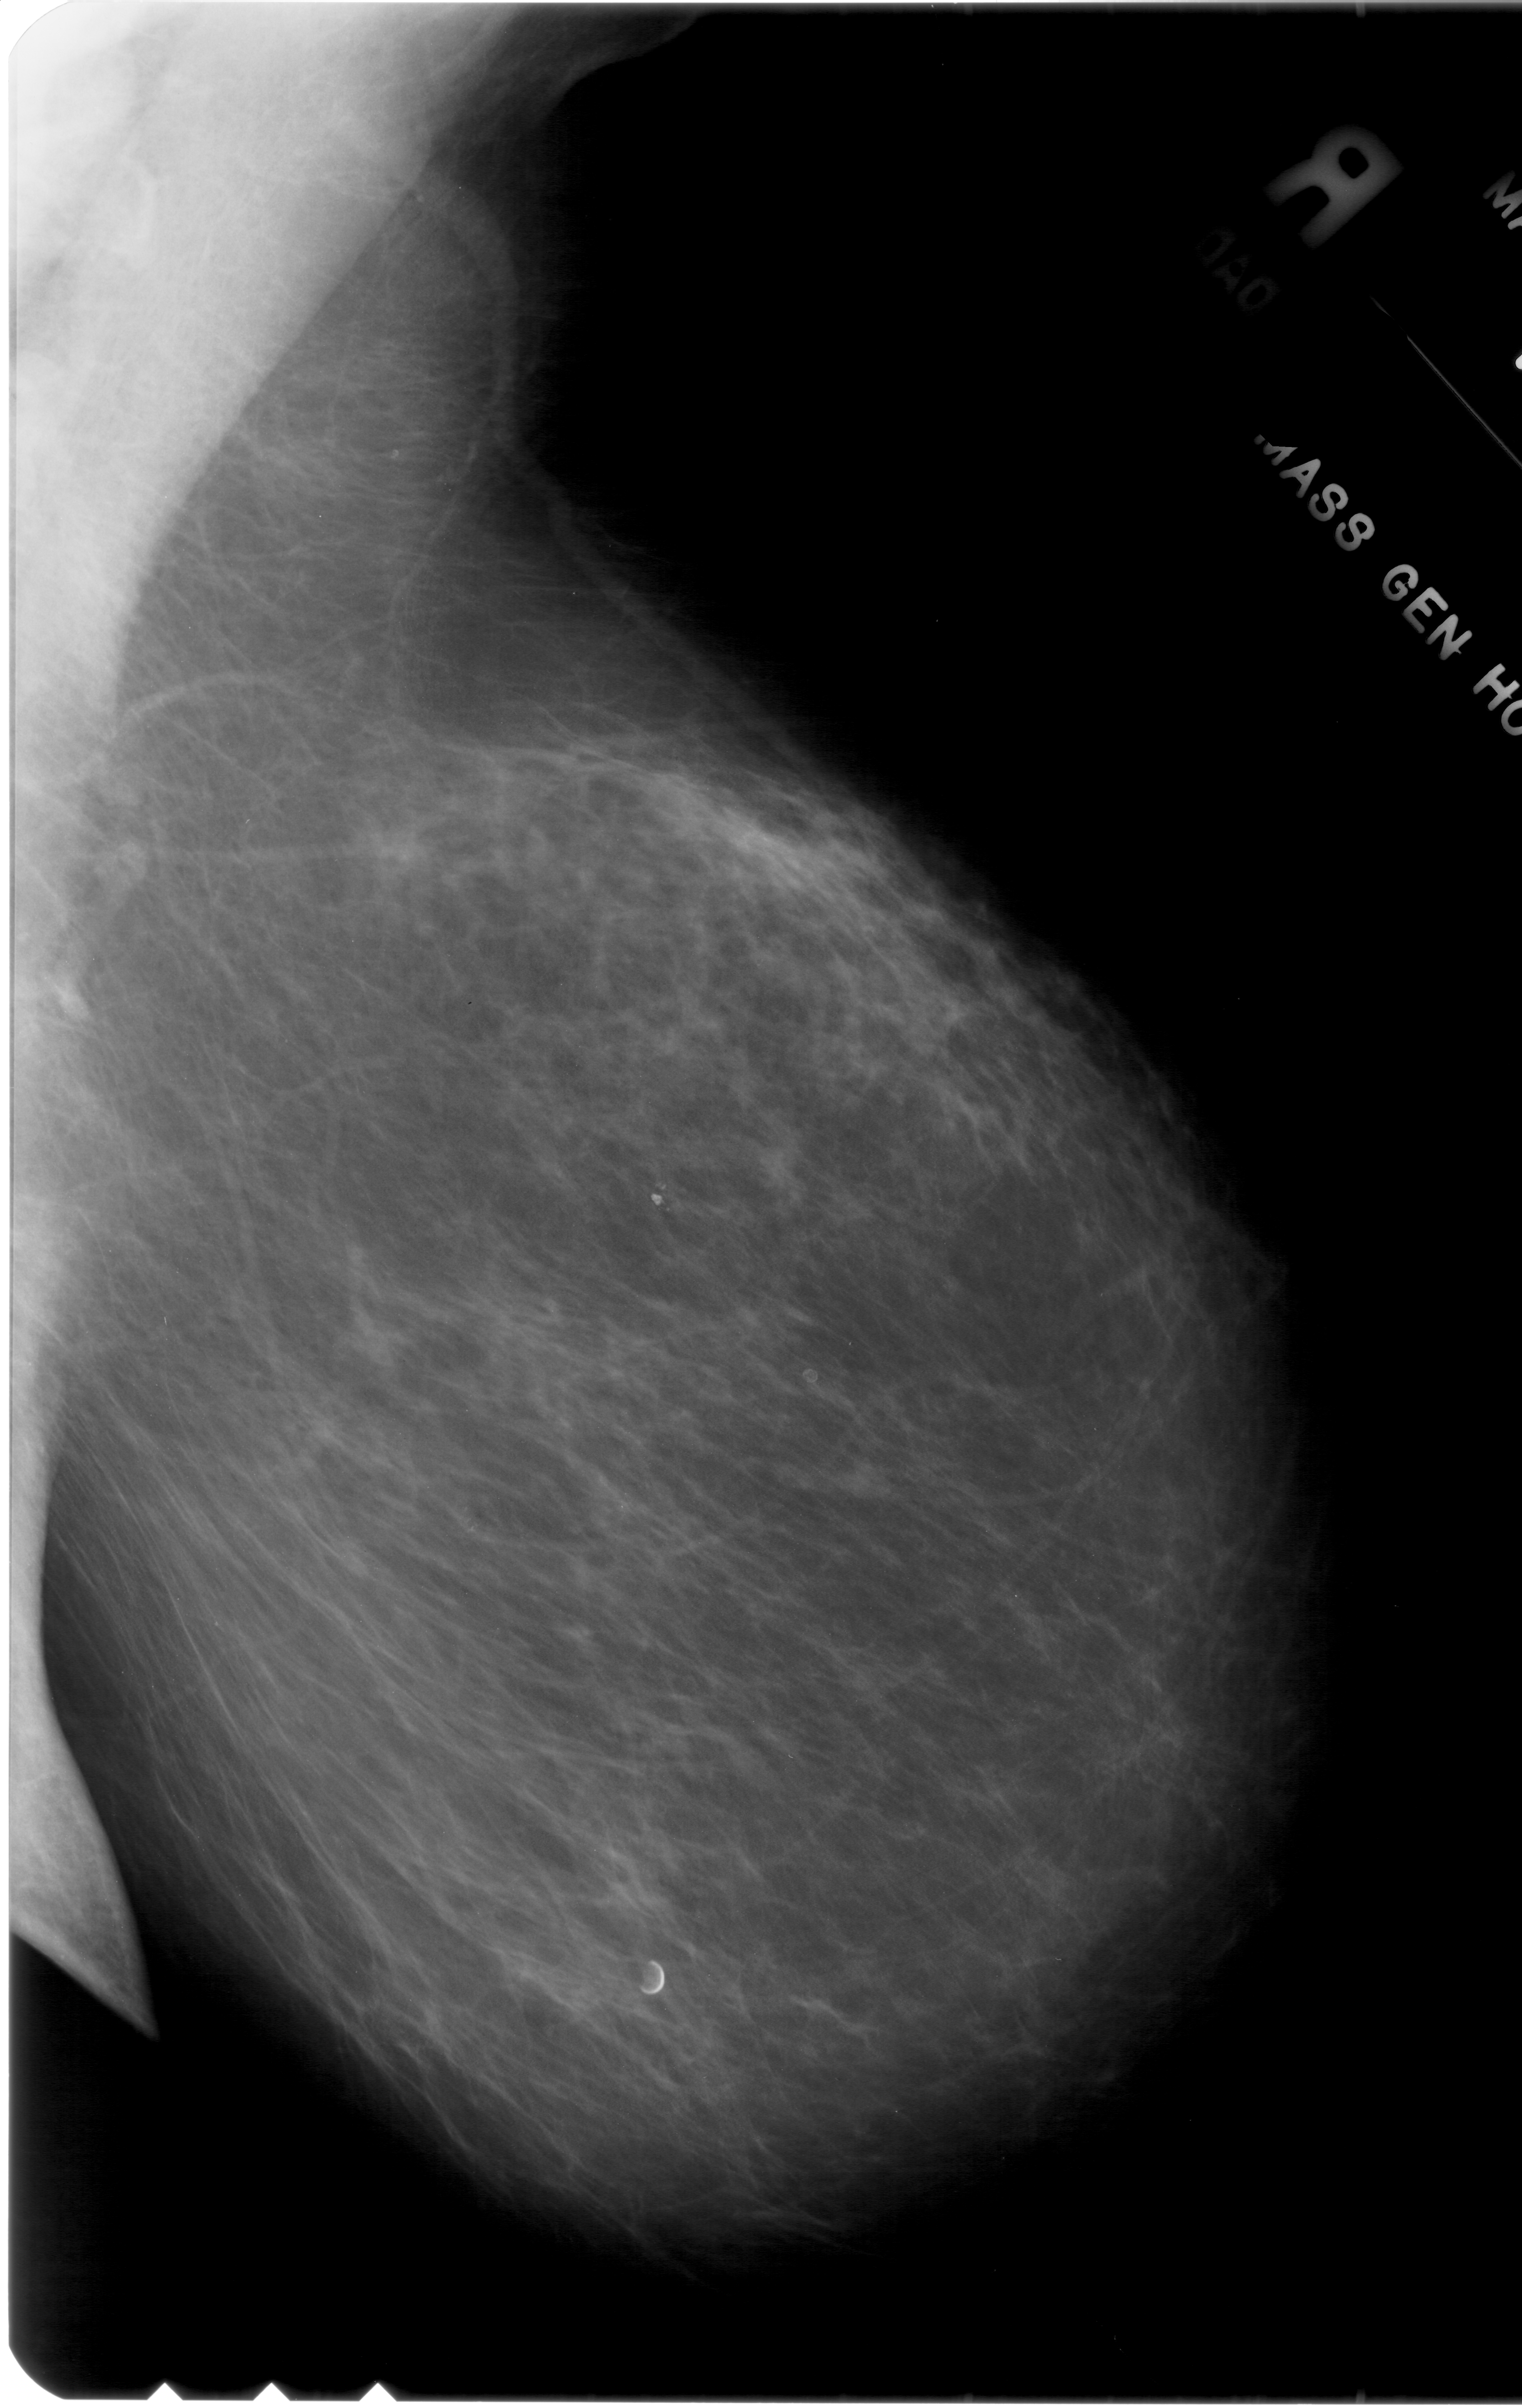
Mammogram (digitized film); right breast; MLO view; BI-RADS breast density category 3 (scale 1–4); 1522 × 2408 image matrix.
Marked abnormalities (boxes around the expert regions of interest):
- calcifications, morphology pleomorphic, distribution clustered; BI-RADS assessment category 4; subtlety rating 2 on a 1 (subtle) to 5 (obvious) scale; pathology result (as recorded, not read from the image): benign: bounding box [x1, y1, x2, y2] px = [428, 1487, 489, 1540]